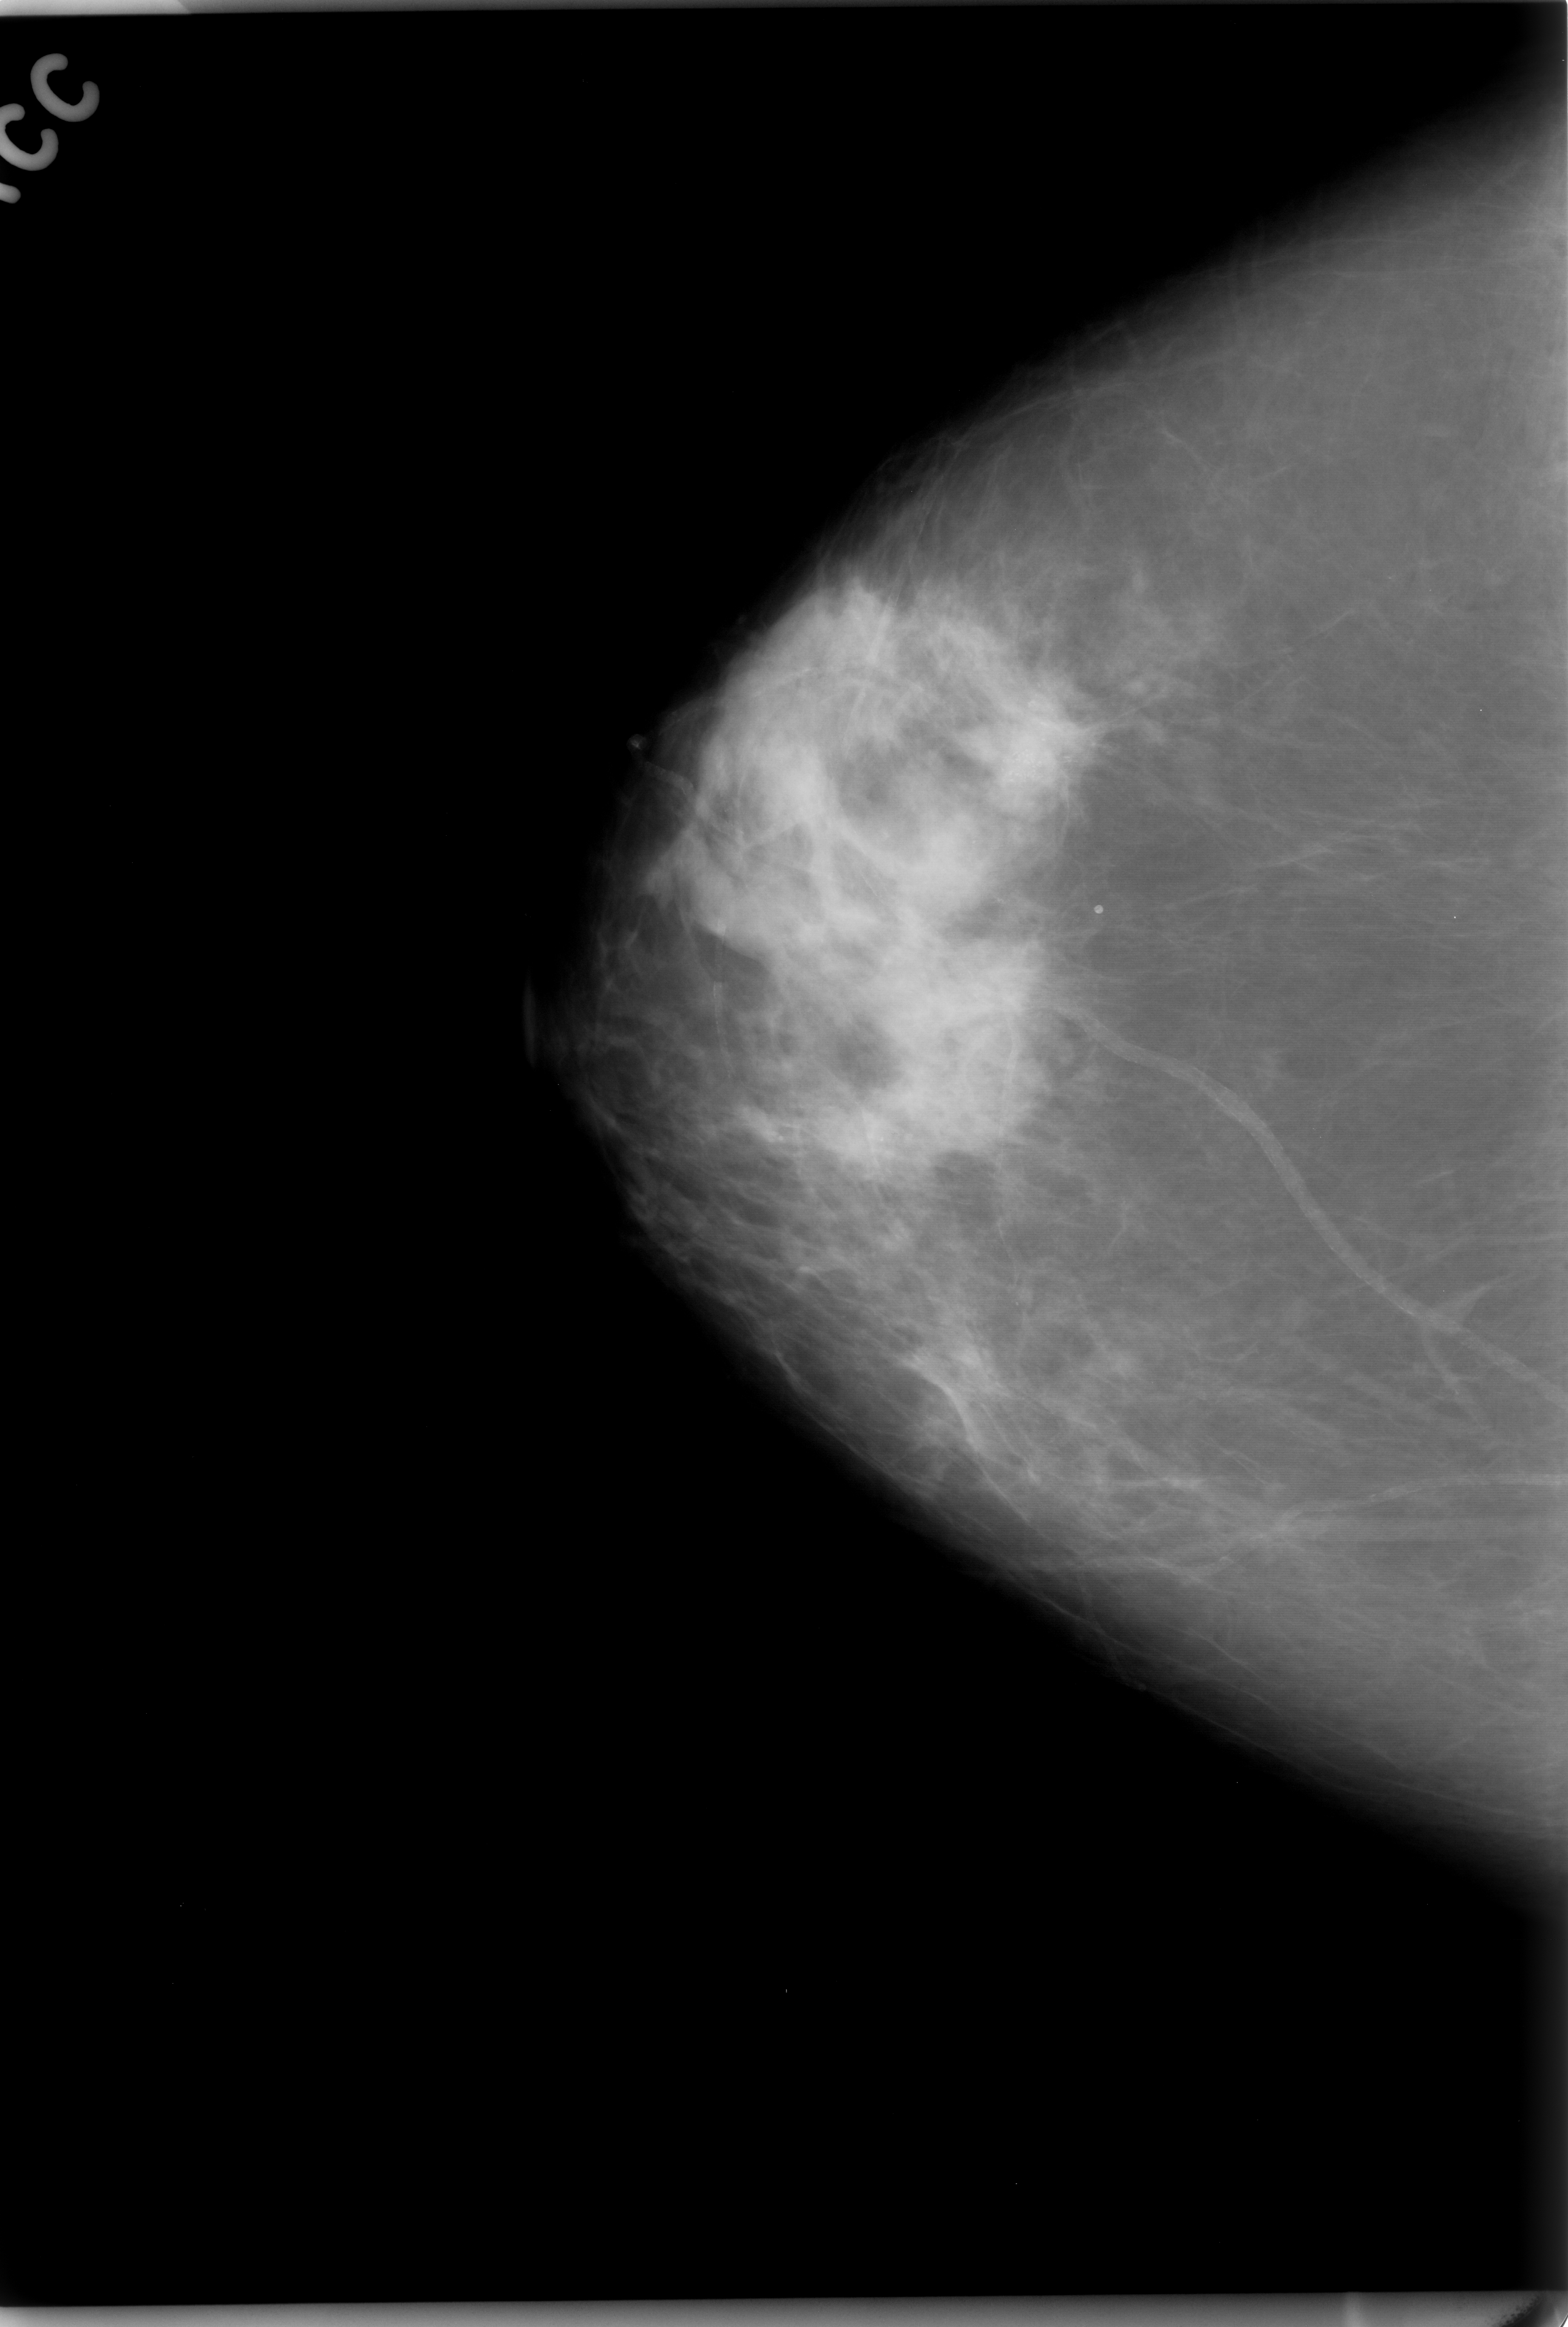
Scanned film-screen mammogram; right breast; CC view; breast composition: scattered fibroglandular densities (BI-RADS density category 2 of 4).
- Abnormality record for this image: calcifications, morphology pleomorphic, distribution clustered; BI-RADS assessment category 5; subtlety rating 4 on a 1 (subtle) to 5 (obvious) scale; pathology (as recorded): malignant.